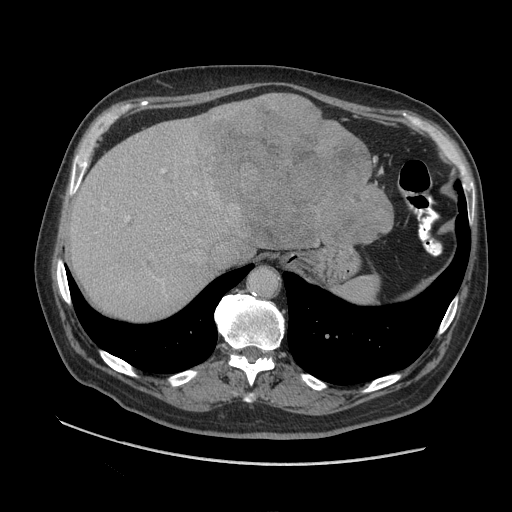
Contrast-enhanced abdominal CT (liver protocol), one axial slice; slice 75 of 109 in the series (ordered by position); reconstruction kernel STANDARD; soft-tissue window (W 400 / L 40 HU); 2.5 mm slice thickness; 512 × 512 image matrix. From the clinical record (not read from this slice): diagnosis: hepatocellular carcinoma (patient treated with transarterial chemoembolisation; whether this scan precedes or follows treatment is not stated here); TNM stage (as recorded): Stage-I; Child-Pugh class: A; tumour nodularity: uninodular.
Outlined on this slice (semi-automatic segmentation, software-assisted and operator-edited):
- abdominal aorta: bounding box <249,267,277,298> (left, top, right, bottom; pixels)
- liver parenchyma outside the tumour (the mass and vessels are separate outlines, so this box may not span the whole liver): <68,106,385,320>
- mass: <189,92,394,253>
- liver vessels: <102,169,196,221>